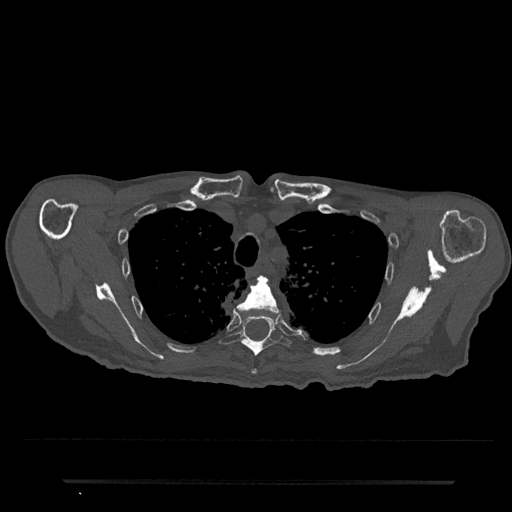
CT including the spine, one axial slice. Slice 593 of 797 in the series (ordered by position). Bone window (W 1800 / L 400 HU). 512 × 512 image matrix, field of view 427 × 427 mm. Male patient, age 74 years. From the clinical record (not read from this slice): primary cancer: prostate.
Outlined on this slice (semi-automatic segmentation, software-assisted and operator-edited):
- T4 vertebra: box from (x=237, y=276) to (x=281, y=375) px
- T5 vertebra: (x=219, y=316)–(x=293, y=356)